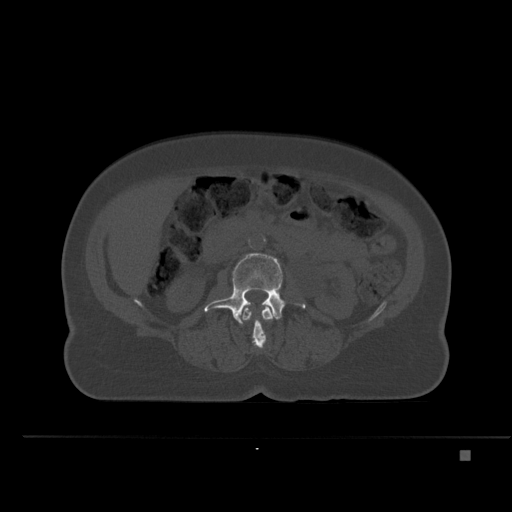
CT including the spine, one axial slice. Position 203 of 477 along the scan axis. Bone window (W 1800 / L 400 HU). 1.5 mm slice thickness. 512 × 512 image matrix, field of view 422 × 422 mm. Female patient, age 74 years. Case-level facts recorded for this patient, not image findings: primary cancer: colon.
Outlined on this slice (semi-automatically segmented with operator editing):
- L2 vertebra: bounding box <242,304,273,349> (left, top, right, bottom; pixels)
- L3 vertebra: <204,253,306,325>